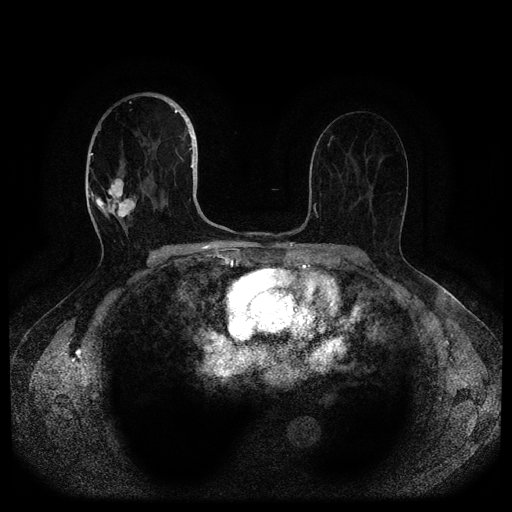
Breast MRI (dynamic contrast-enhanced, multi-phase), one axial slice. Position 57 of 116 along the scan axis. Dynamic contrast-enhanced series, time point 2 of 5 at this slice position (early post-contrast). 1.5 T. TE 2.6 ms, TR 5.3 ms. 2 mm slice thickness. 512 × 512 image matrix. Patient: female, 82 years.
Annotated regions visible in this slice (semi-automatically segmented with operator editing):
- breast lesion (labelled 'tumour' in the annotation; benign lesions carry a separate 'benign' label): bounding box <100,178,137,220> (left, top, right, bottom; pixels)